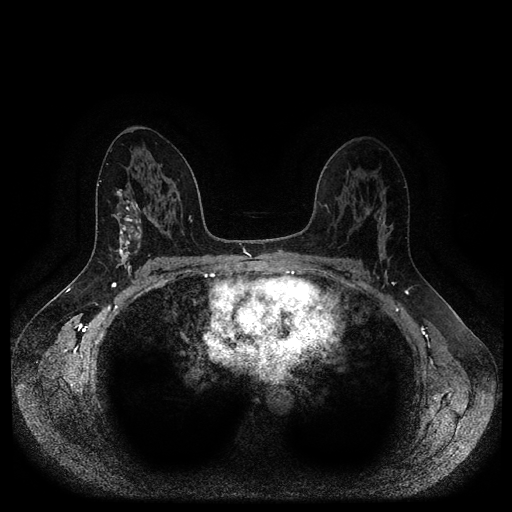
Breast MRI (dynamic contrast-enhanced, multi-phase), one axial slice; position 59 of 116 along the scan axis; dynamic contrast-enhanced series, time point 2 of 5 at this slice position (early post-contrast); 1.5 T; TE 2.6 ms, TR 5.3 ms; 2 mm slice thickness; 512 × 512 image matrix, field of view 360 × 360 mm. Patient: female, 45 years.
Structures marked on this image (semi-automatically segmented with operator editing):
- breast lesion (labelled benign in the annotation): bounding box (x1, y1, x2, y2) in pixels: (113, 189, 145, 276)